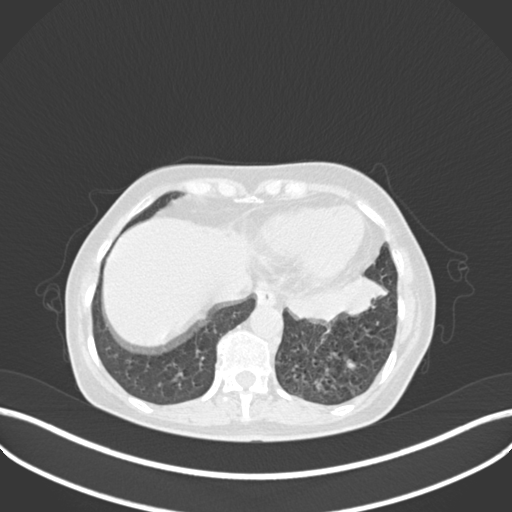
Chest CT, one axial slice; position 57 of 270 along the scan axis; reconstruction kernel B30f; lung window (W 1500 / L -600 HU); 512 × 512 image matrix, field of view 400 × 400 mm. Female patient, age 63 years. From the clinical record (not read from this slice): clinical TNM (as recorded): T1b N0 M0.
Structures marked on this image (rectangle marked by the reading radiologist):
- lung tumour (recorded histology: adenocarcinoma): box from (x=284, y=265) to (x=390, y=326) px